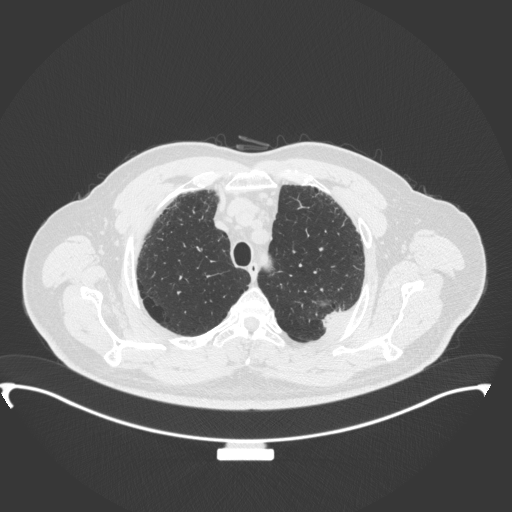
Chest CT, one axial slice. Slice 294 of 350 in the series (ordered by position). Lung window (W 1500 / L -600 HU). 512 × 512 image matrix. Male patient, age 64 years. Case-level facts recorded for this patient, not image findings: clinical TNM (as recorded): T1c N1 M1.
Structures marked on this image (bounding box drawn by a radiologist):
- lung tumour (recorded histology: adenocarcinoma): bounding box (x1, y1, x2, y2) in pixels: (316, 305, 348, 331)